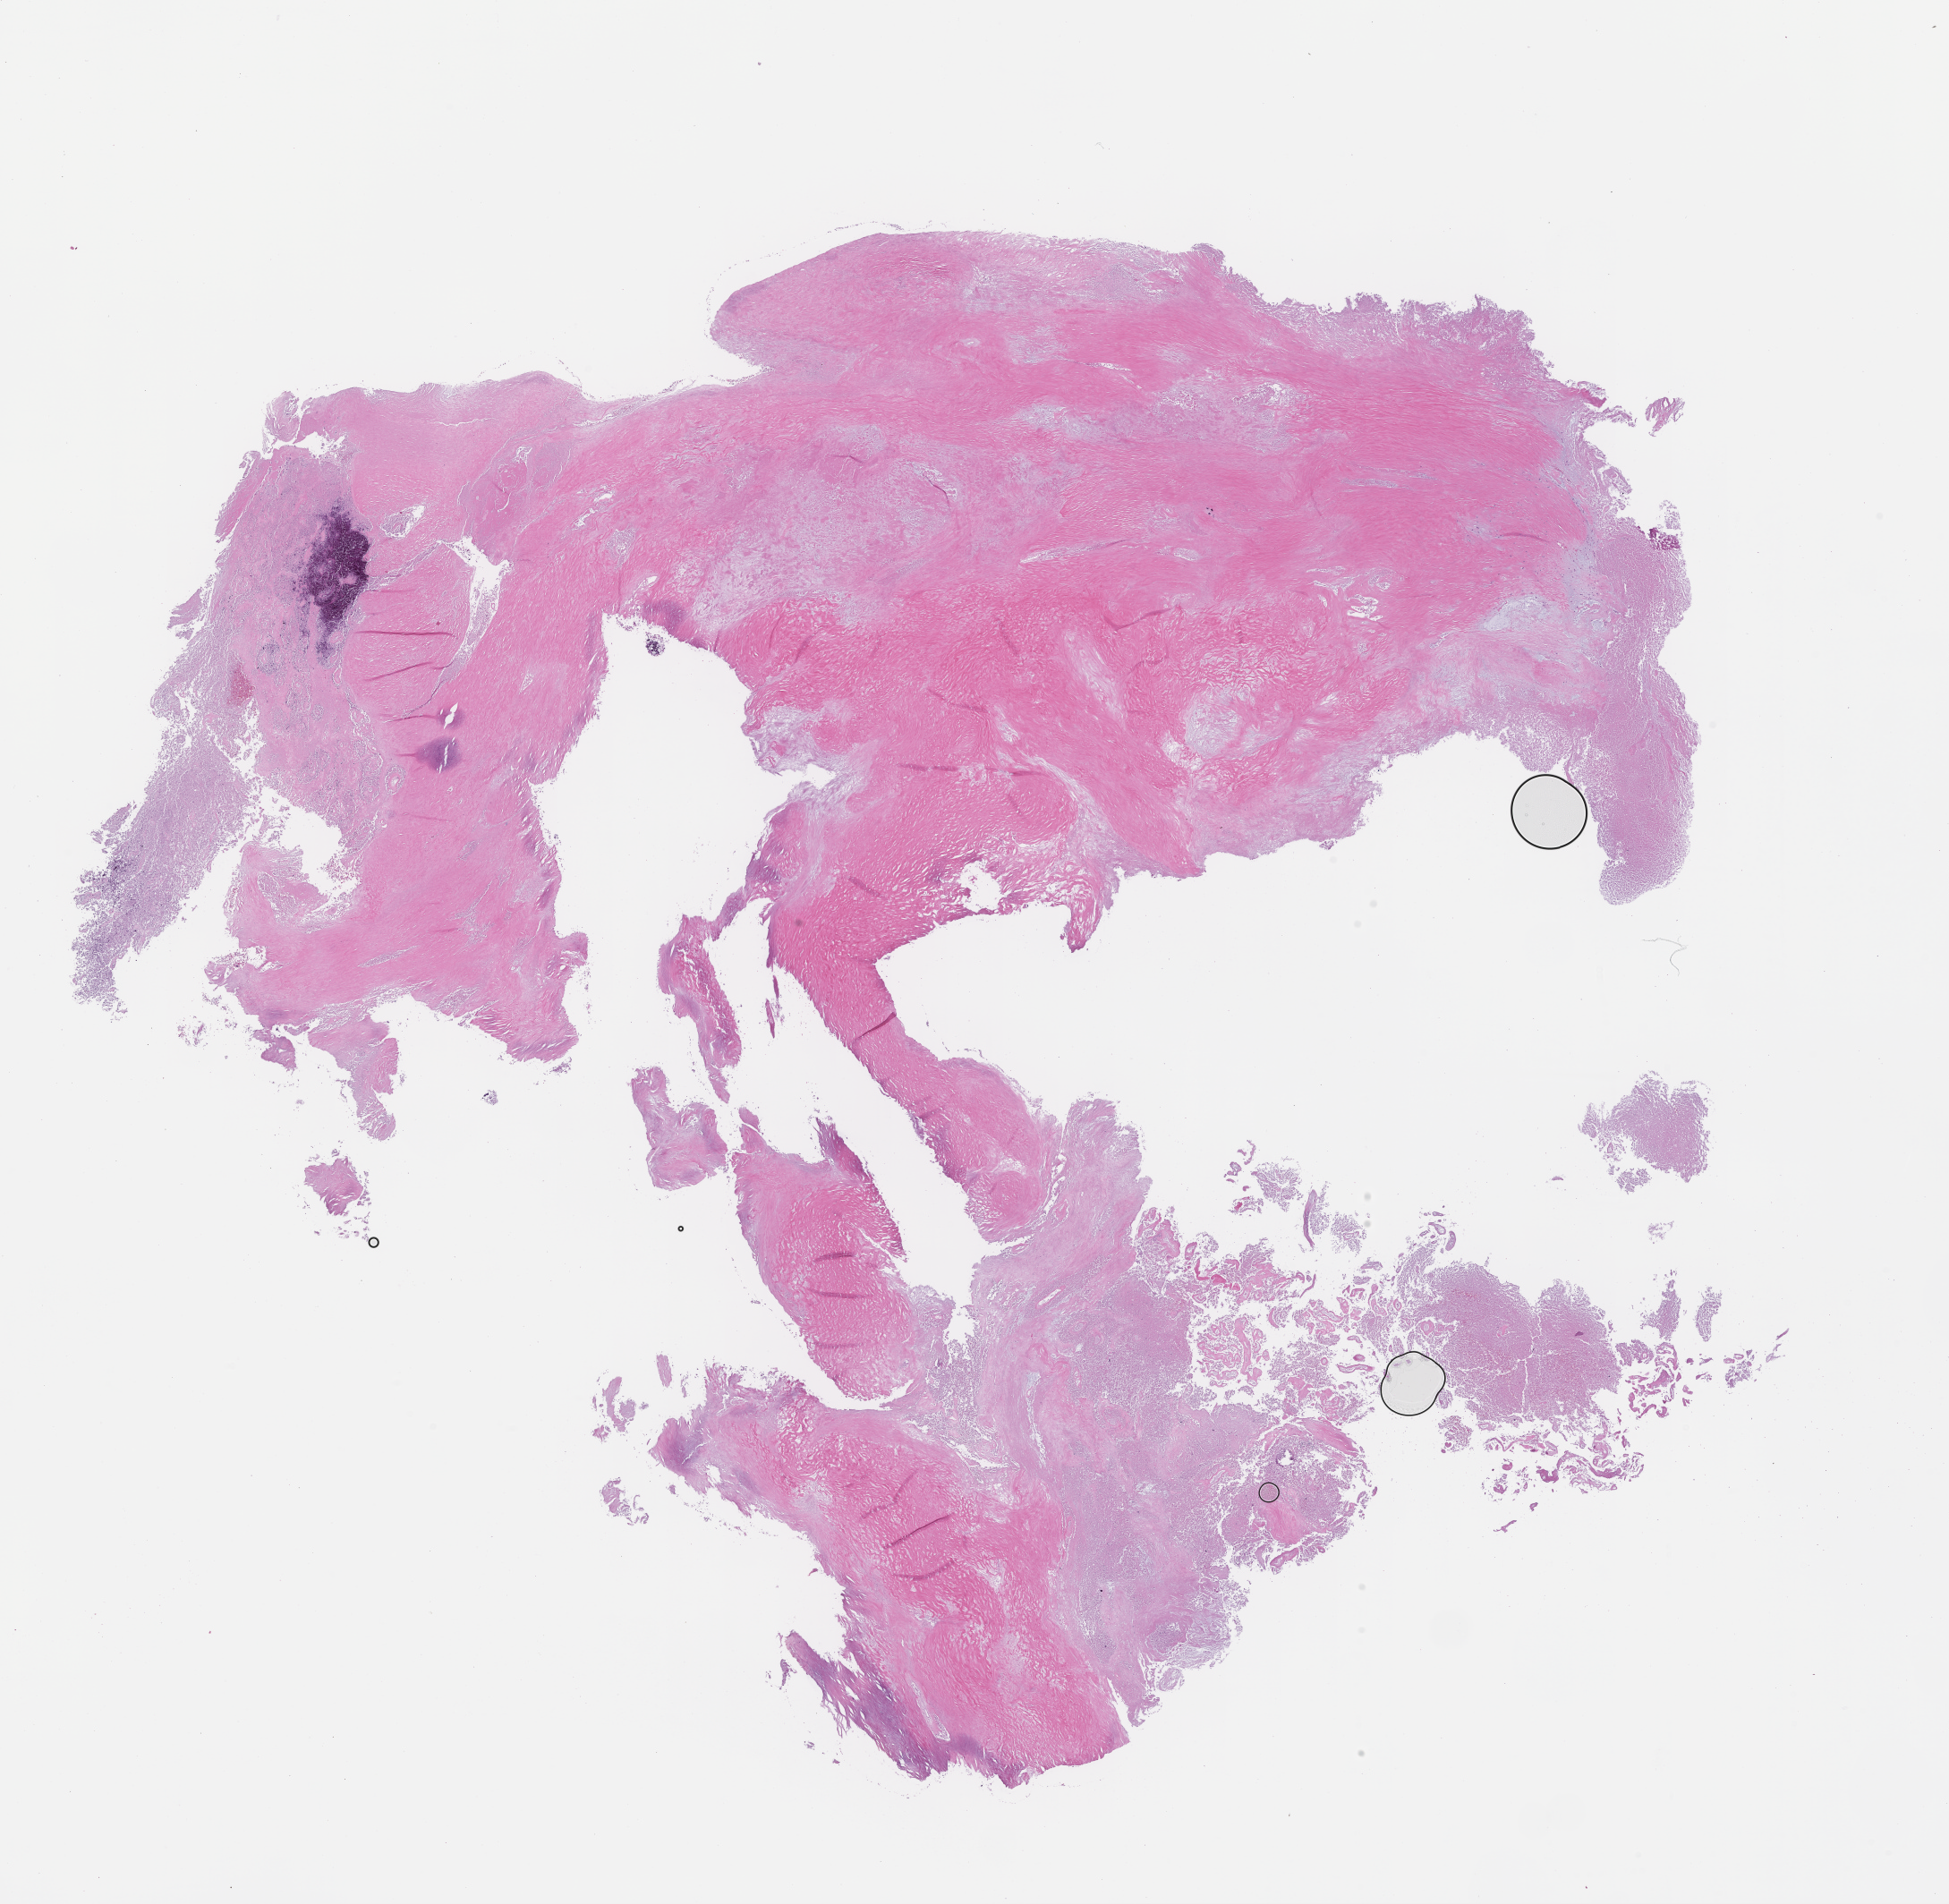
Whole-slide image, hematoxylin and eosin (H&E) stain, shown as a low-resolution overview of the whole scanned area (about 17.6 x 17.2 mm), FFPE section, tissue site: ovary, specimen time point: collected at baseline (before treatment). Patient: female.
* this section: primary tumor
* diagnosis: Ovarian Carcinoma